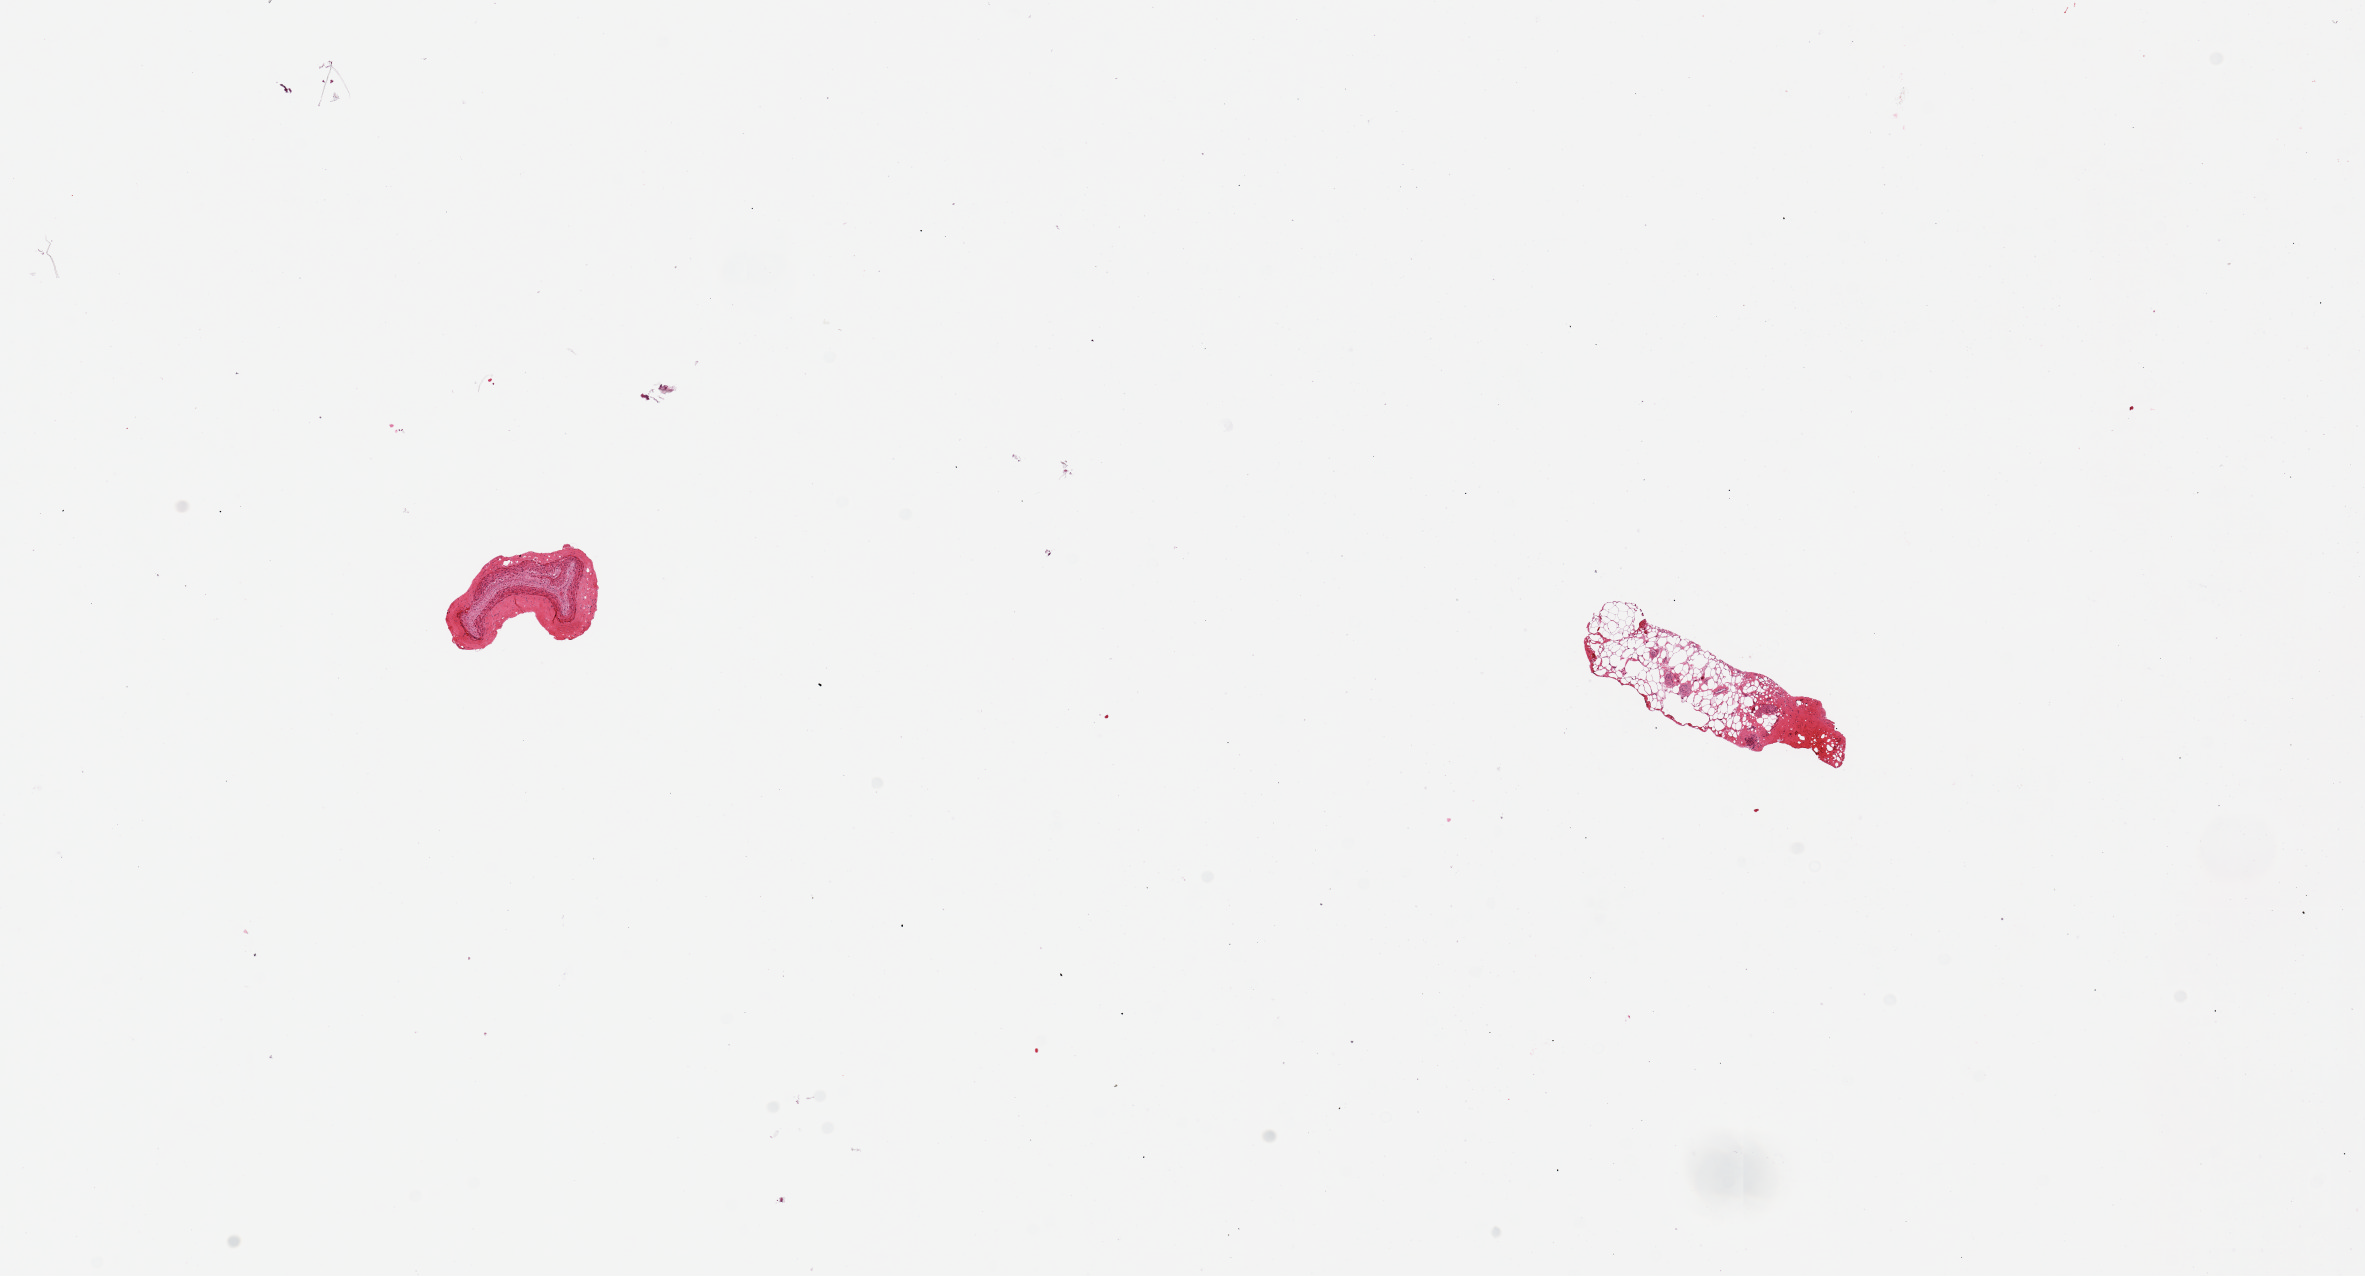
Whole-slide image, haematoxylin and eosin stain, brightfield, shown as a low-resolution overview of the whole scanned area (about 18.7 x 10.1 mm). PAXgene-fixed, paraffin-embedded tissue. Sampled site (target tissue): coronary artery. Donor tissue sample.
* reviewer comment on this tissue sample: 2 pieces: 1 is a small (1mm) artery; other is a 2x0.5mm fatty piece with focal hemorrhage